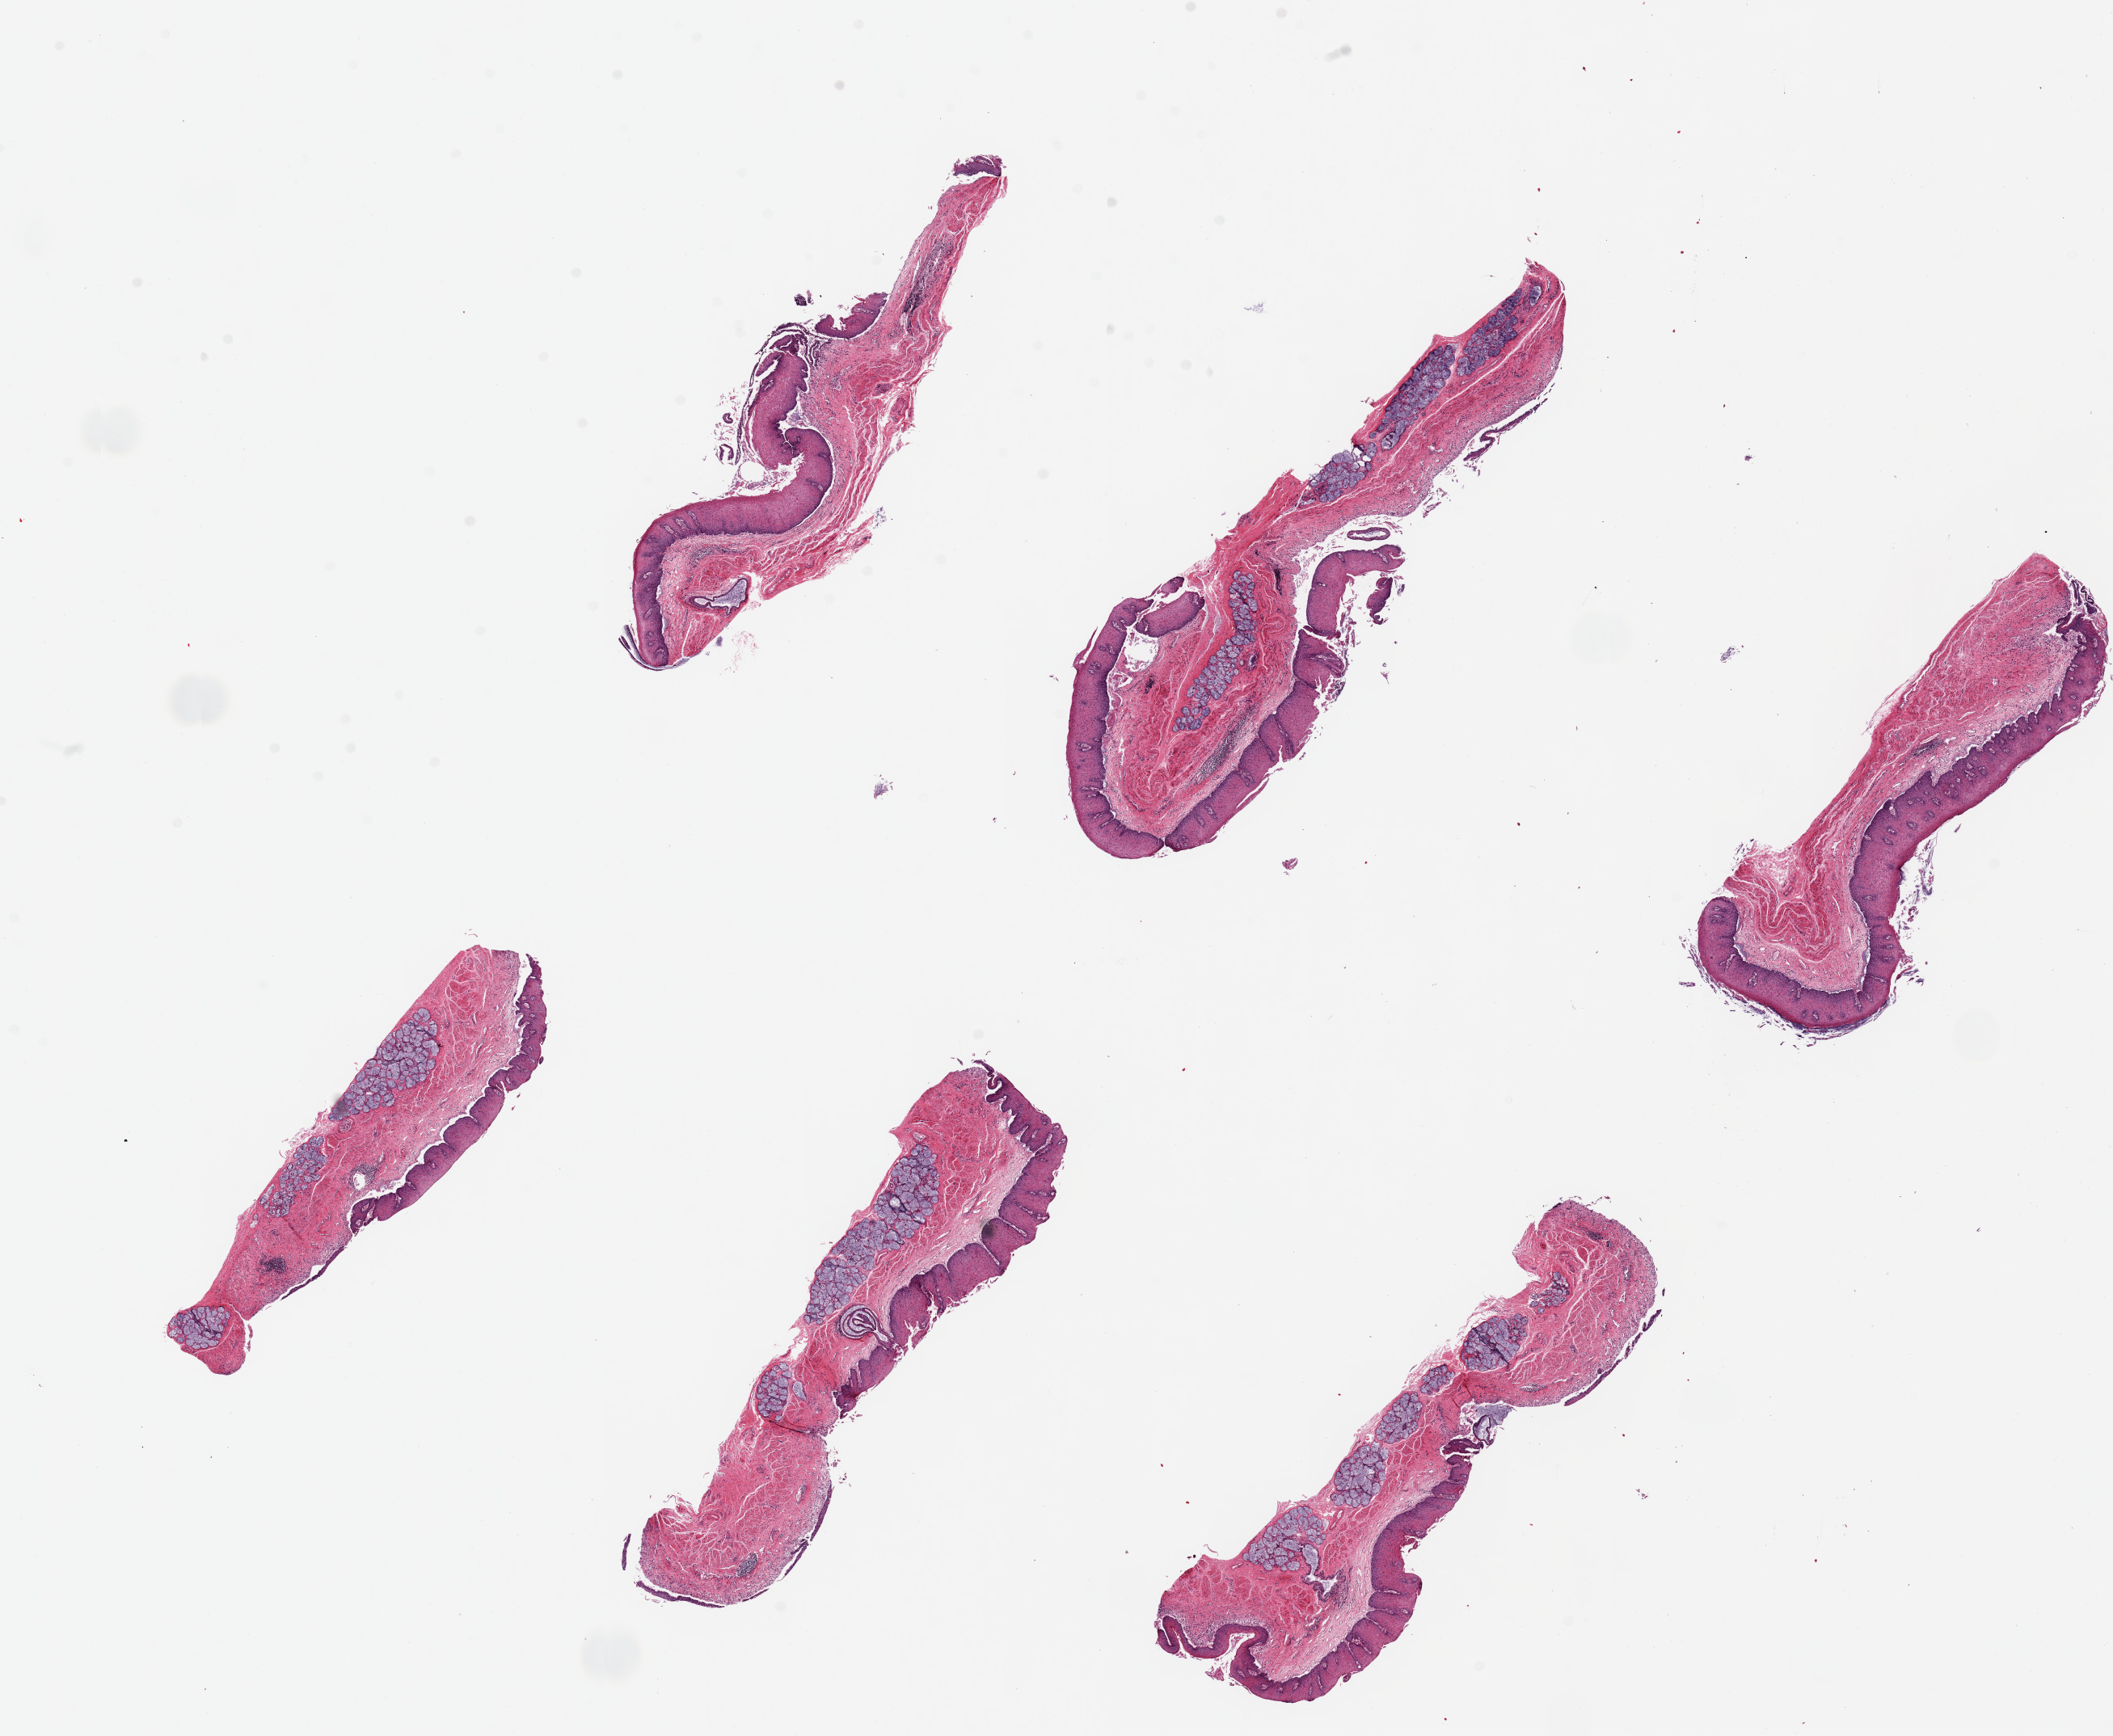
Hematoxylin and eosin (H&E) whole-slide image — whole scanned area (about 20.7 x 17.0 mm, from a 20x scan) shown as a low-resolution overview. PAXgene-fixed, paraffin-embedded tissue. Sampled site (target tissue): esophageal mucous membrane. Tissue donor sample. Donor: male.
Review note (as recorded): 6 pieces, up to 7x2mm; Well dissected mucosa with some epithelial detachment.